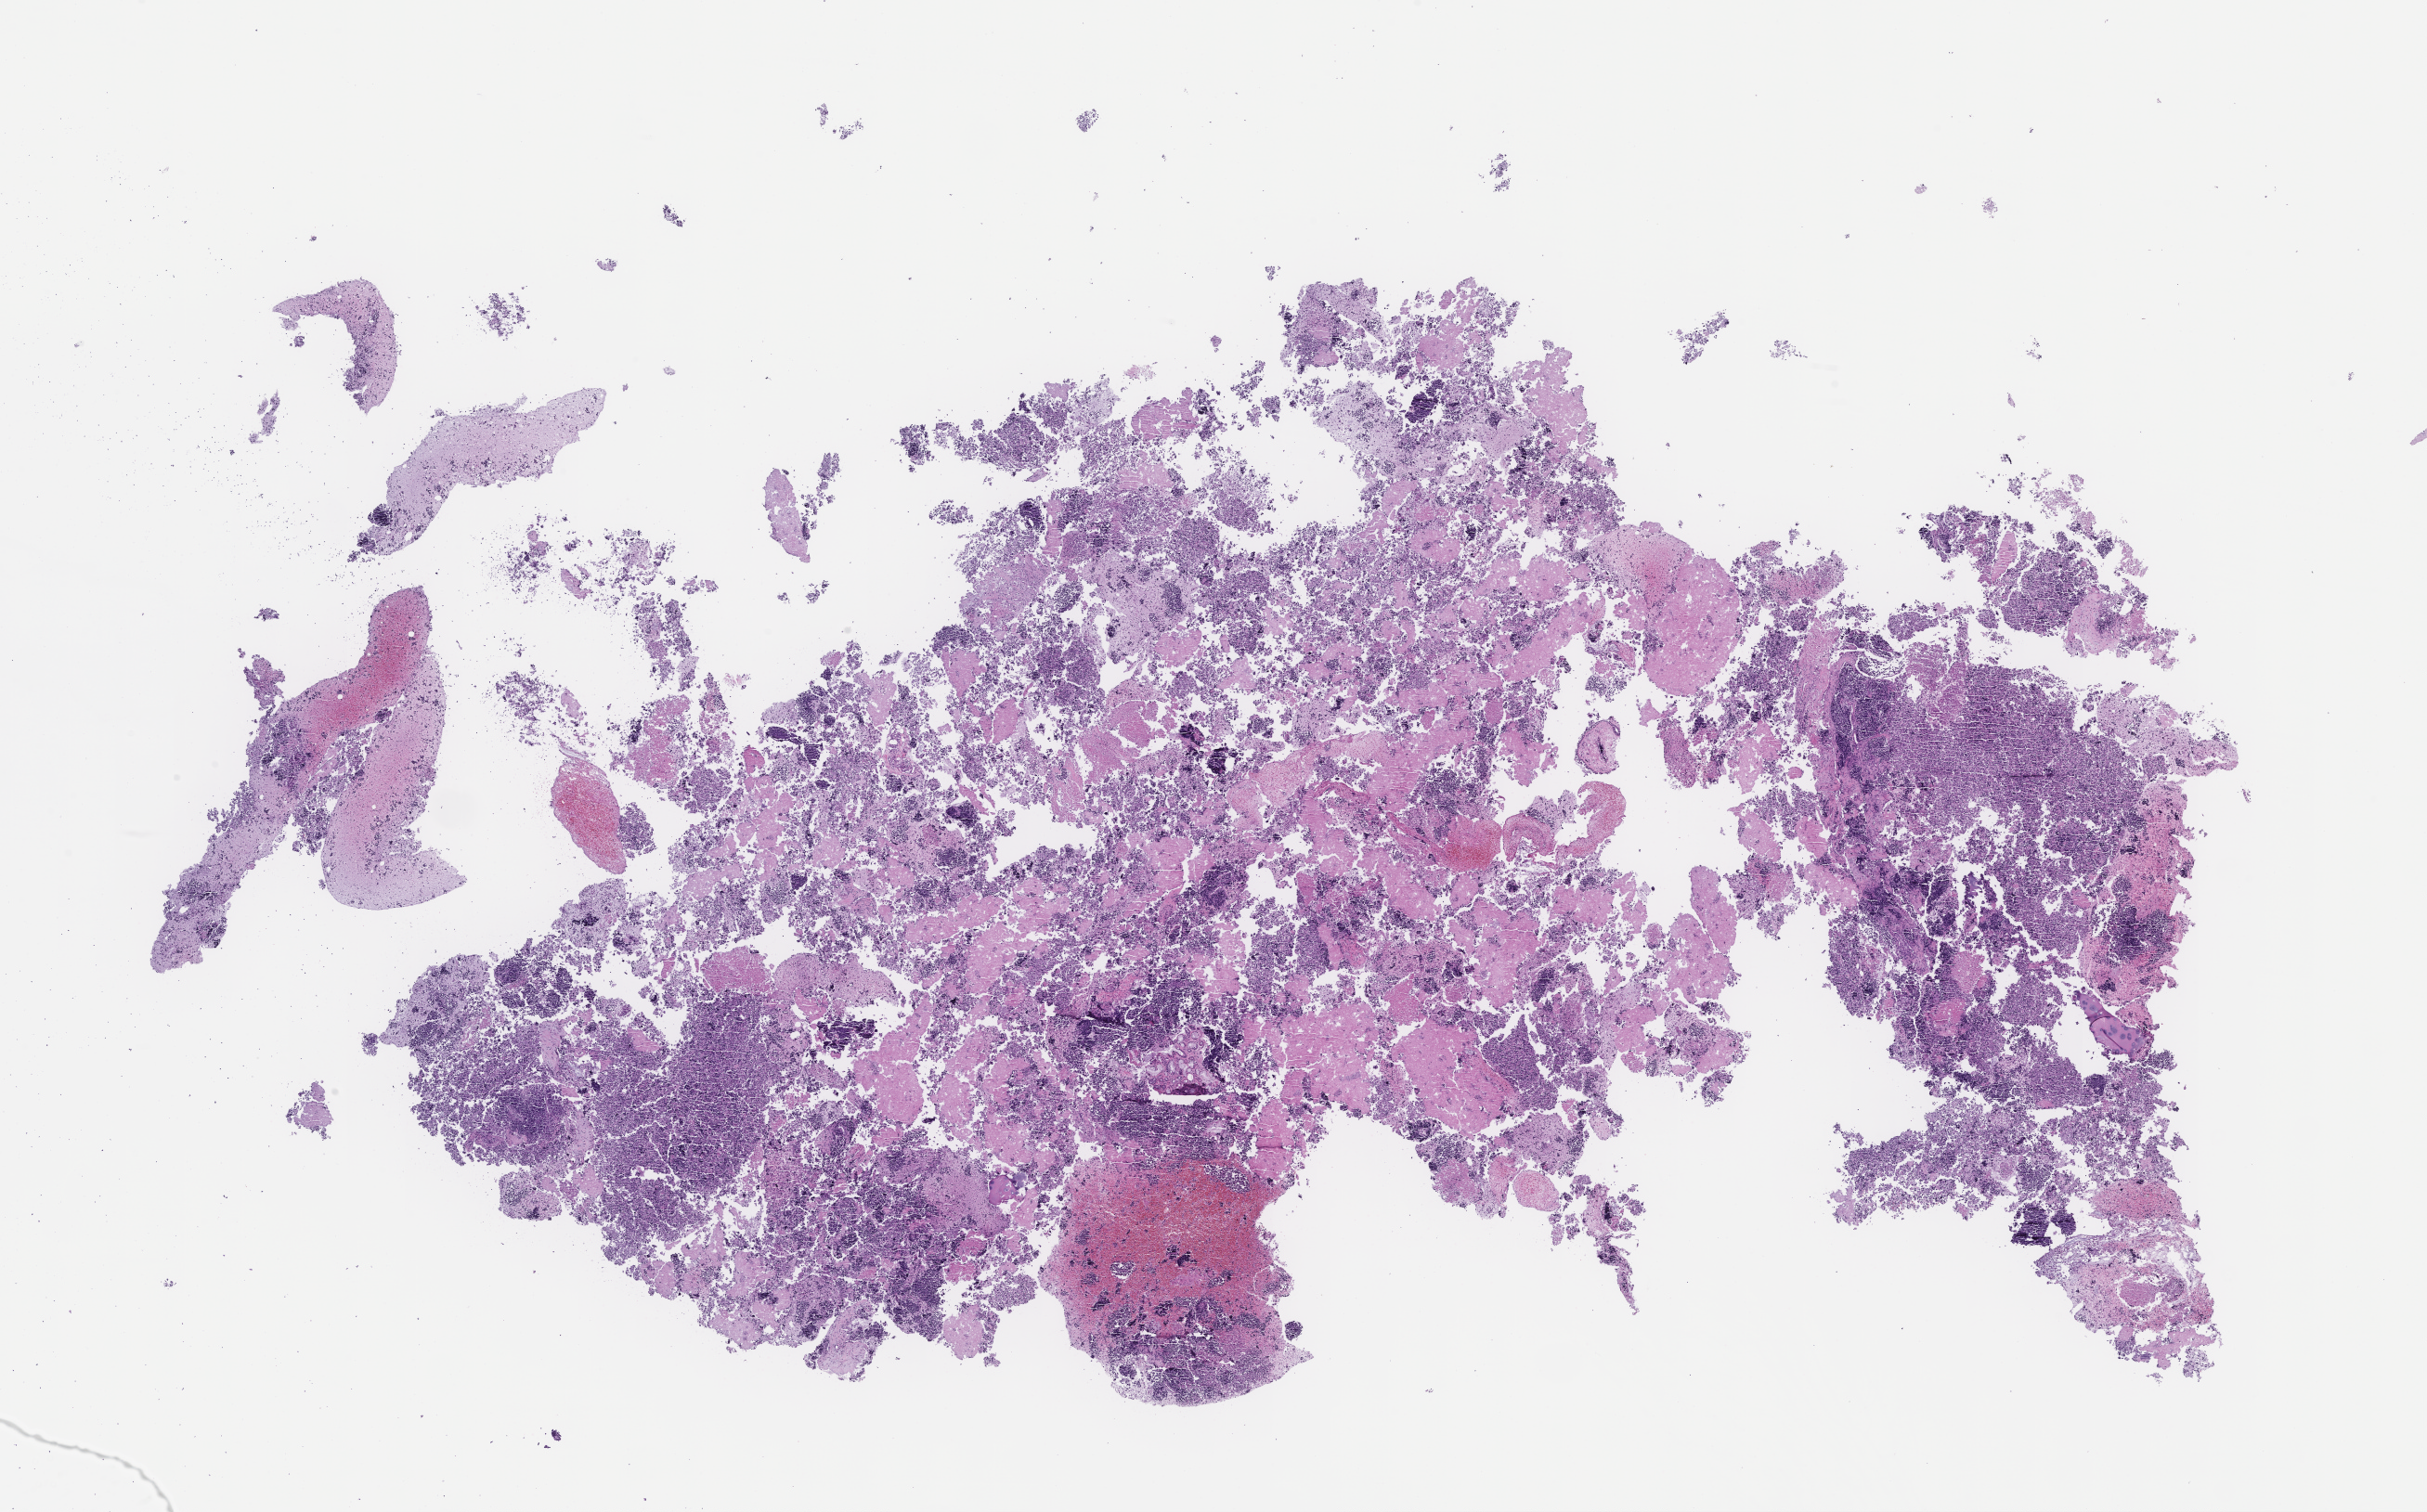
Whole-slide image, H&E stain — a low-resolution overview of the entire scanned area, about 21.1 x 13.2 mm. Formalin-fixed paraffin-embedded section. Site: lung. Archival tissue. Patient sex: female.
- this section: primary tumour tissue
- diagnosis: Small Cell Lung Carcinoma